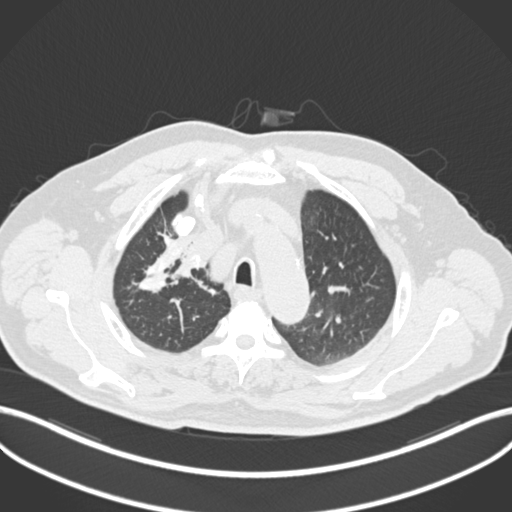
Chest CT, one axial slice. Slice 161 of 255 in the series (ordered by position). 120 kVp. Lung window (W 1500 / L -600 HU). 1 mm slice thickness. 512 × 512 image matrix. Patient: male, 60 years. From the clinical record (not read from this slice): clinical TNM (as recorded): T1b N1 M0.
Outlined on this slice (rectangle marked by the reading radiologist):
- lung tumour (recorded histology: squamous cell carcinoma): bounding box [x1, y1, x2, y2] px = [171, 252, 207, 289]